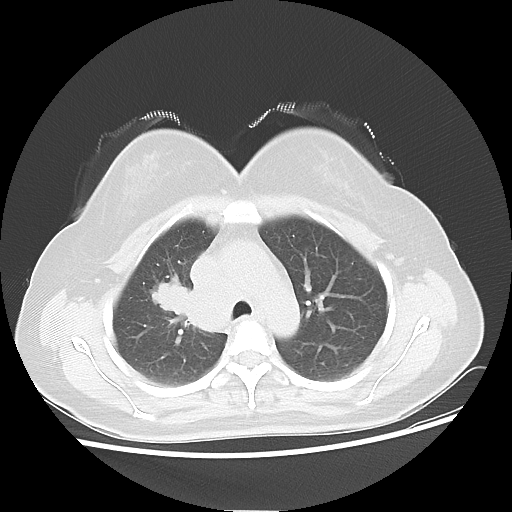
Chest CT, one axial slice; slice 36 of 50 in the series (ordered by position); lung window (W 1500 / L -600 HU); 5 mm slice thickness; 512 × 512 image matrix, field of view 360 × 360 mm. Female patient, age 40 years. From the clinical record (not read from this slice): clinical TNM (as recorded): T1c N3 M0.
Outlined on this slice (rectangle marked by the reading radiologist):
- lung tumour (recorded histology: small cell carcinoma): bounding box <140,269,185,315> (left, top, right, bottom; pixels)